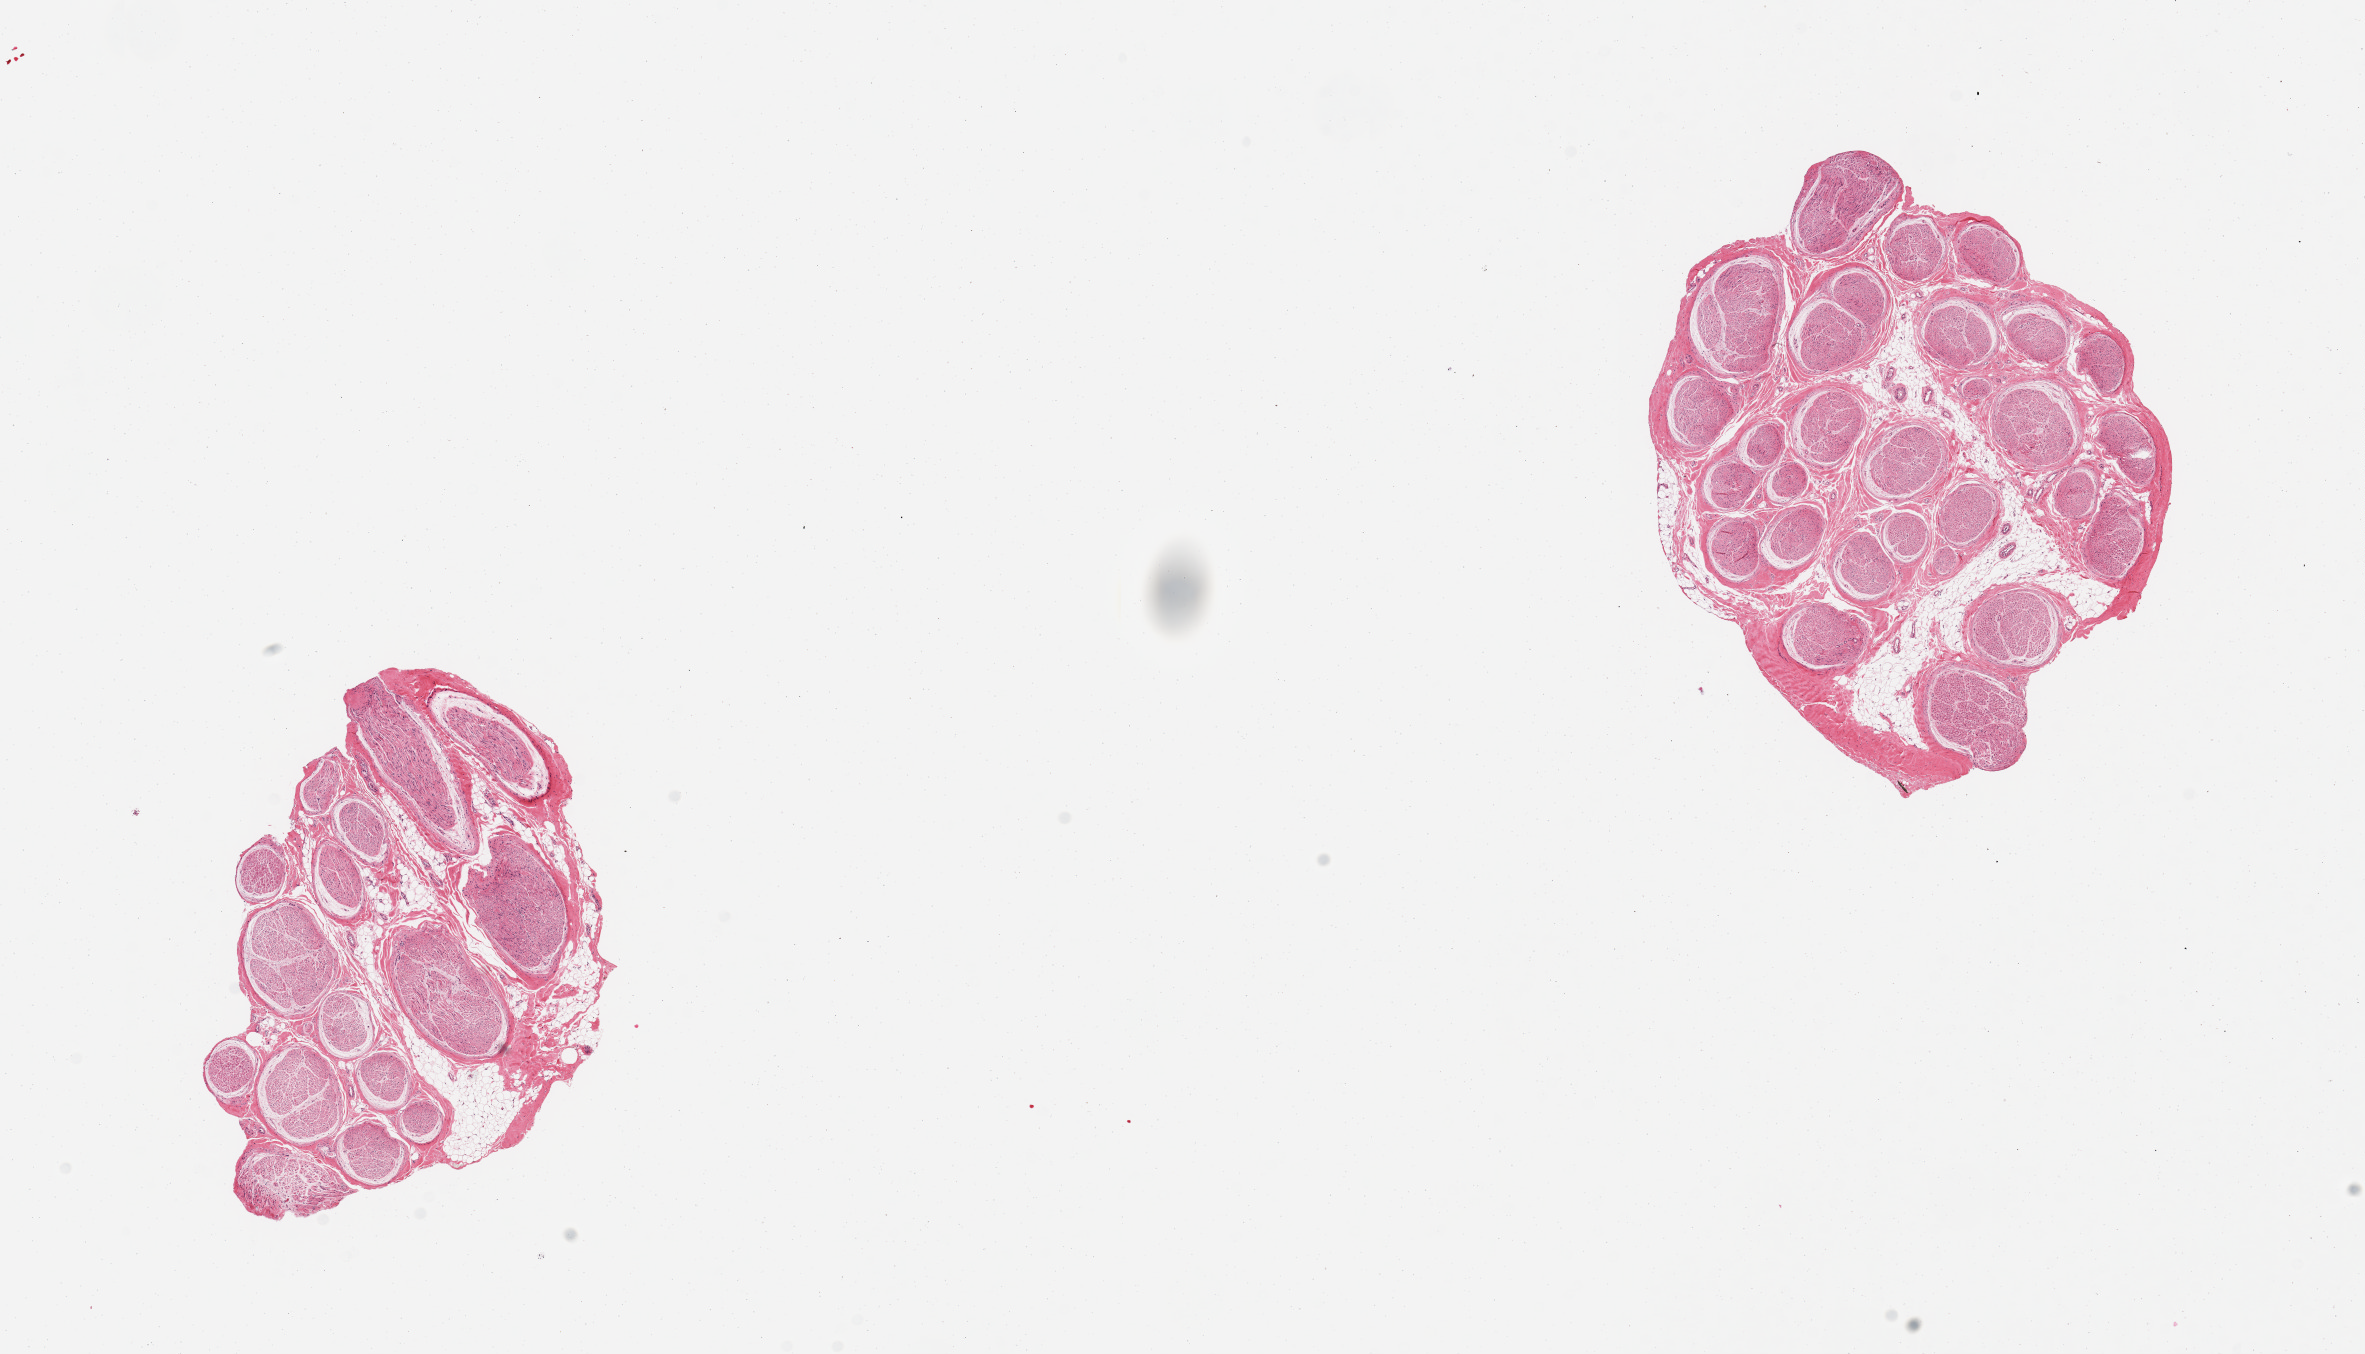
Whole-slide image, H&E stain, shown as a low-resolution overview of the whole scanned area (about 18.7 x 10.7 mm); PAXgene-fixed, paraffin-embedded tissue; target tissue: tibial nerve; tissue donor sample. Male donor.
Pathologist's review note for this sample: 2 pieces, good clean specimens.